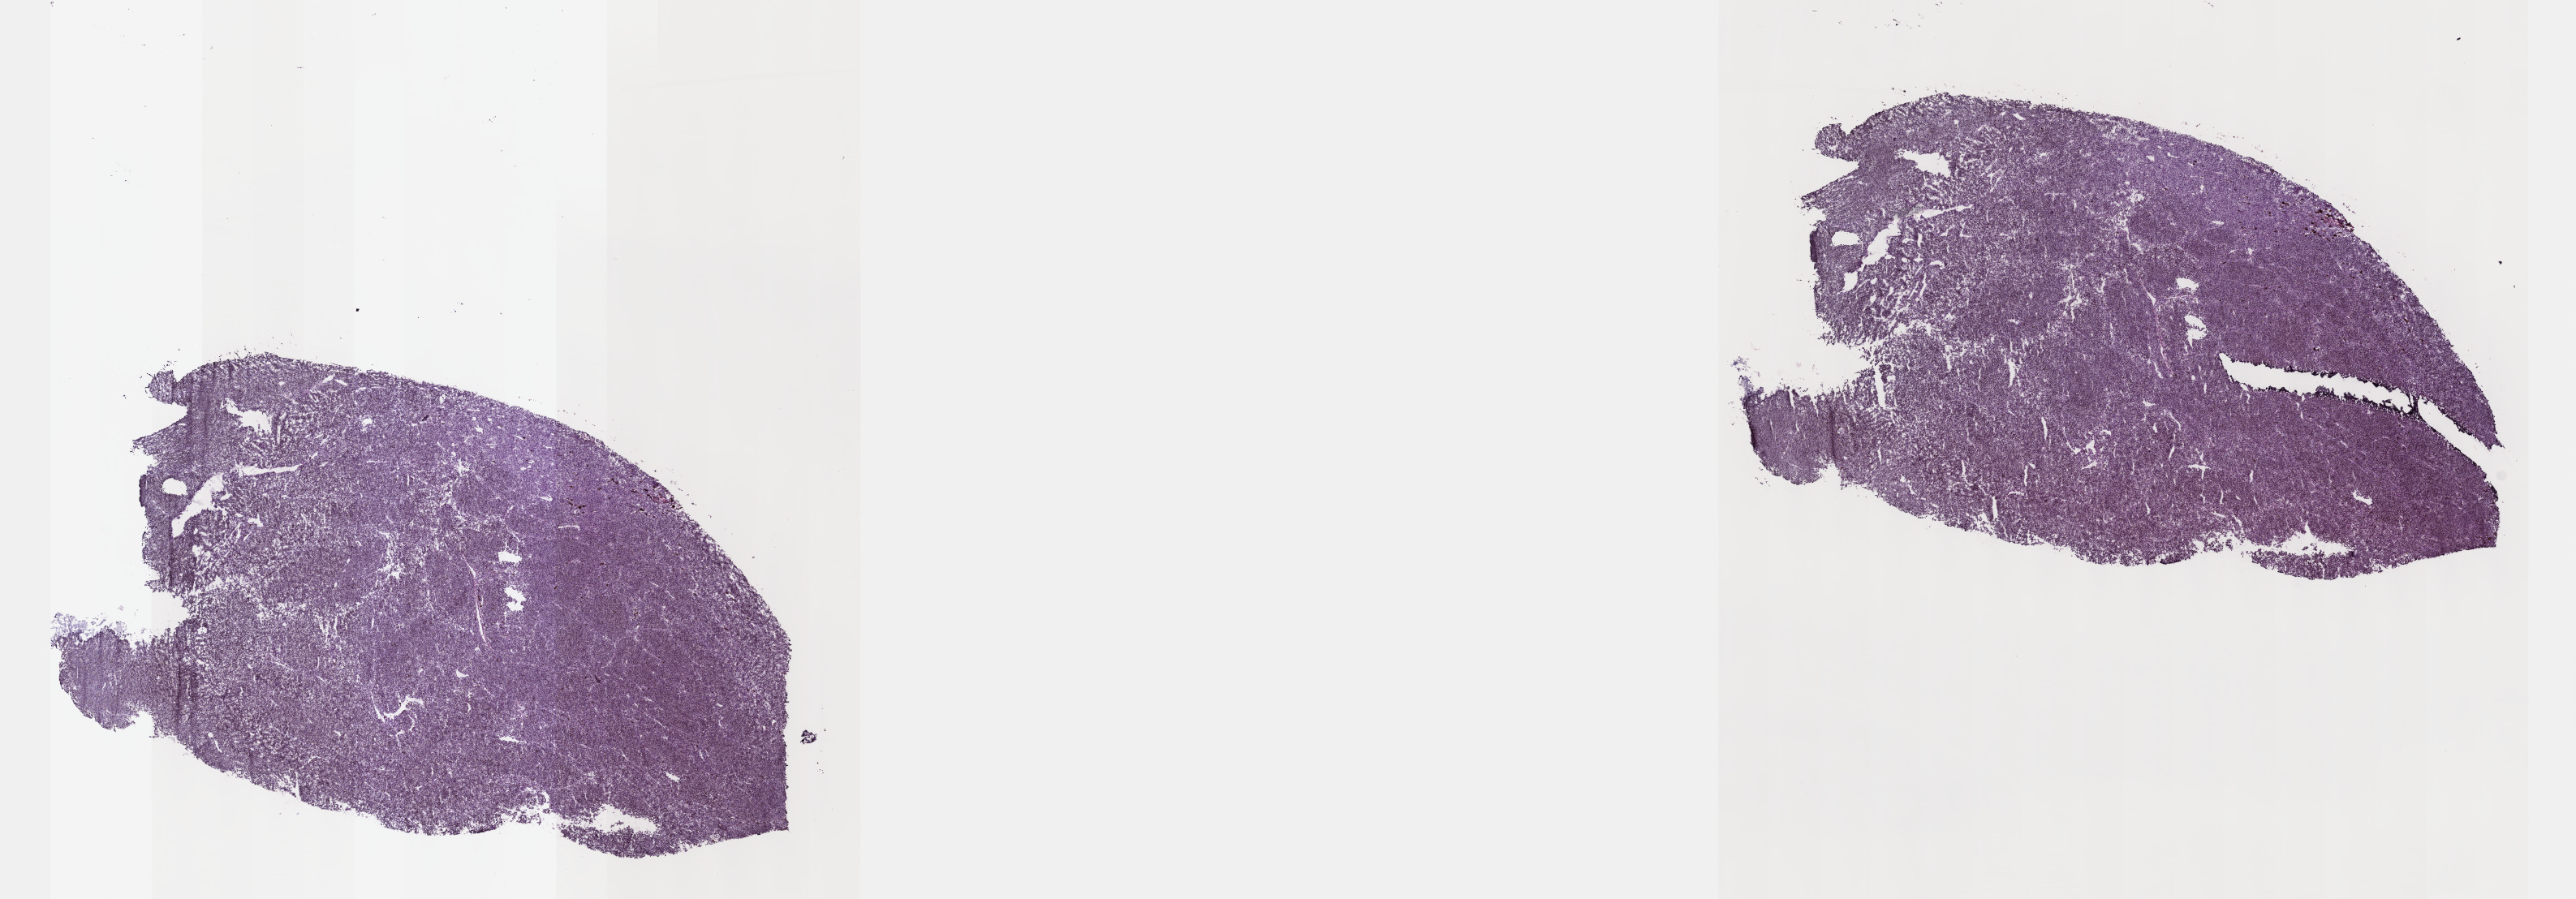
Digitized H&E-stained tissue section (whole slide), a low-resolution overview of the entire scanned area, about 25.7 x 9.0 mm (acquisition: 40x scan). Frozen section from the top of the tissue portion. Uvea, primary tumour sample. Female patient; age at initial diagnosis 64 years.
Pathologic diagnosis: Spindle cell melanoma, type B (choroid).